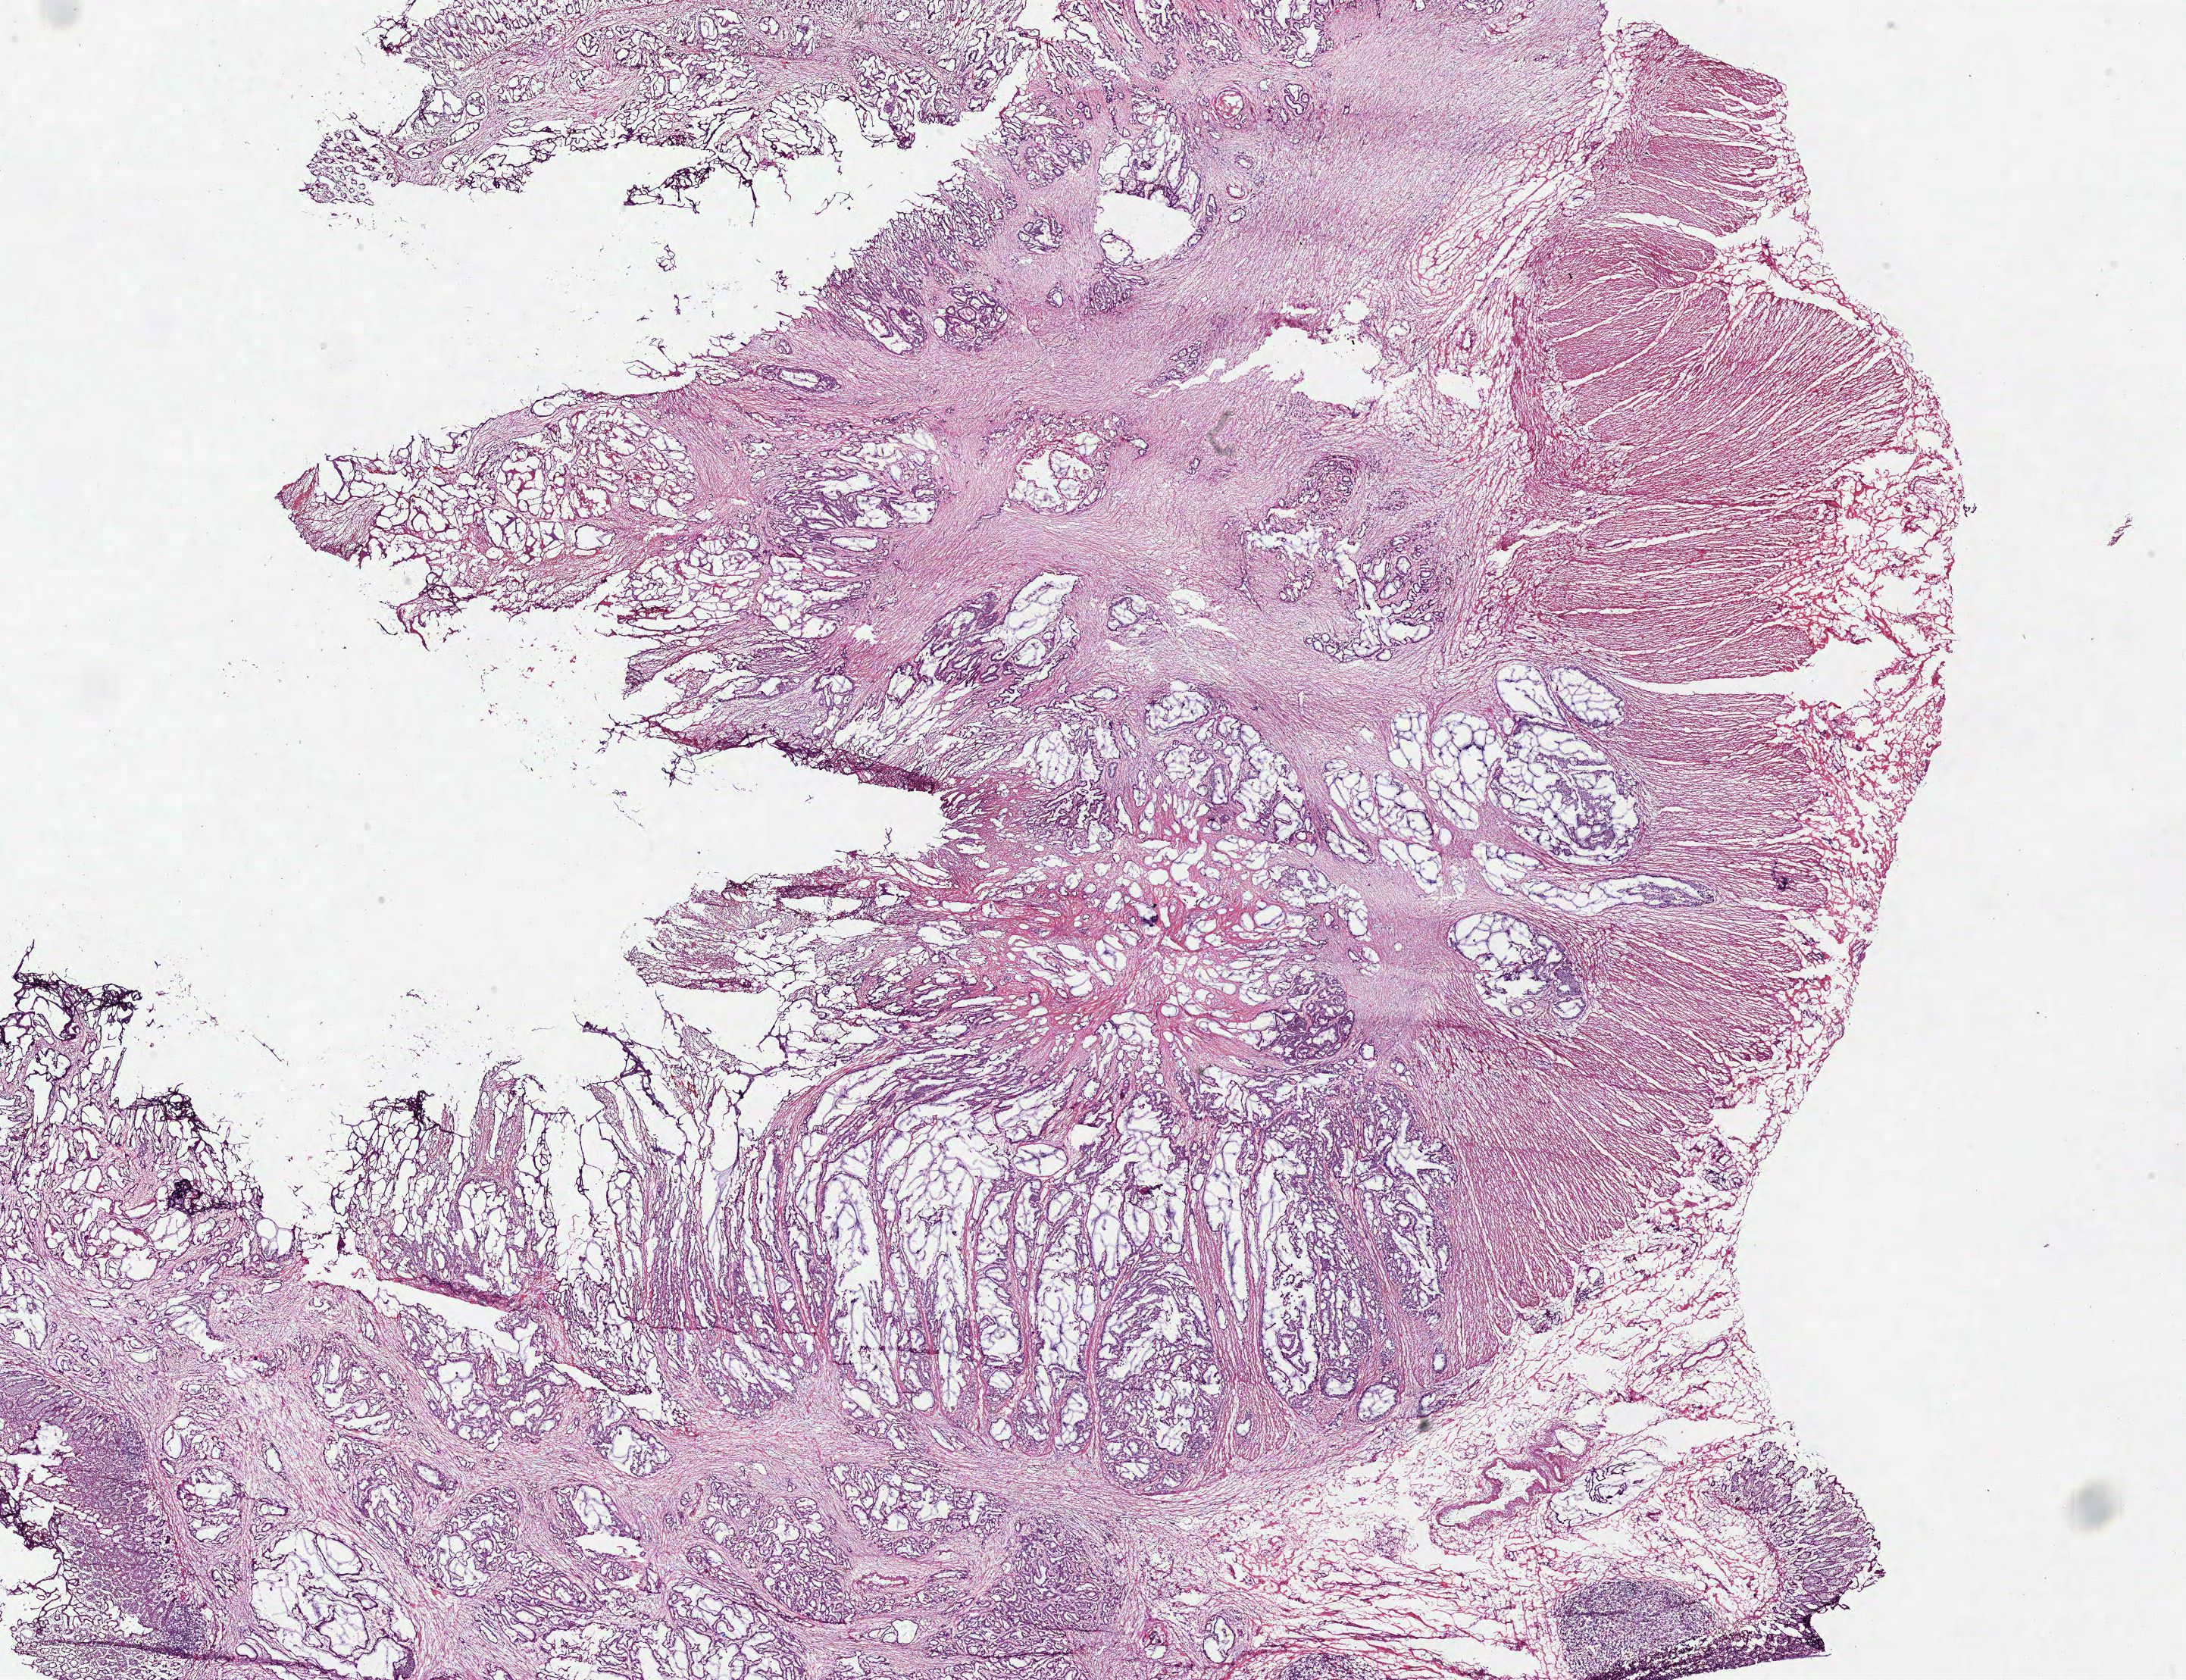
Whole-slide histology image, H&E, low-resolution overview of the scanned area, about 22.7 x 17.5 mm (acquisition: 40x scan); frozen section from the bottom of the tissue portion; sample: primary tumour, colon. Female patient; age at initial diagnosis 41 years. Composition of this section per pathologist review: tumour cells 70%, tumour nuclei 80%, normal cells 7%, stromal cells 20%, necrosis 3%. Infiltration values recorded for this section: lymphocyte infiltration 10%, monocyte infiltration 0%, neutrophil infiltration 0%.
AJCC pathologic stage: IIIC (7th edition). Diagnosis: Adenocarcinoma, NOS. Lymph nodes positive (case pathology): 5 of 5 examined.